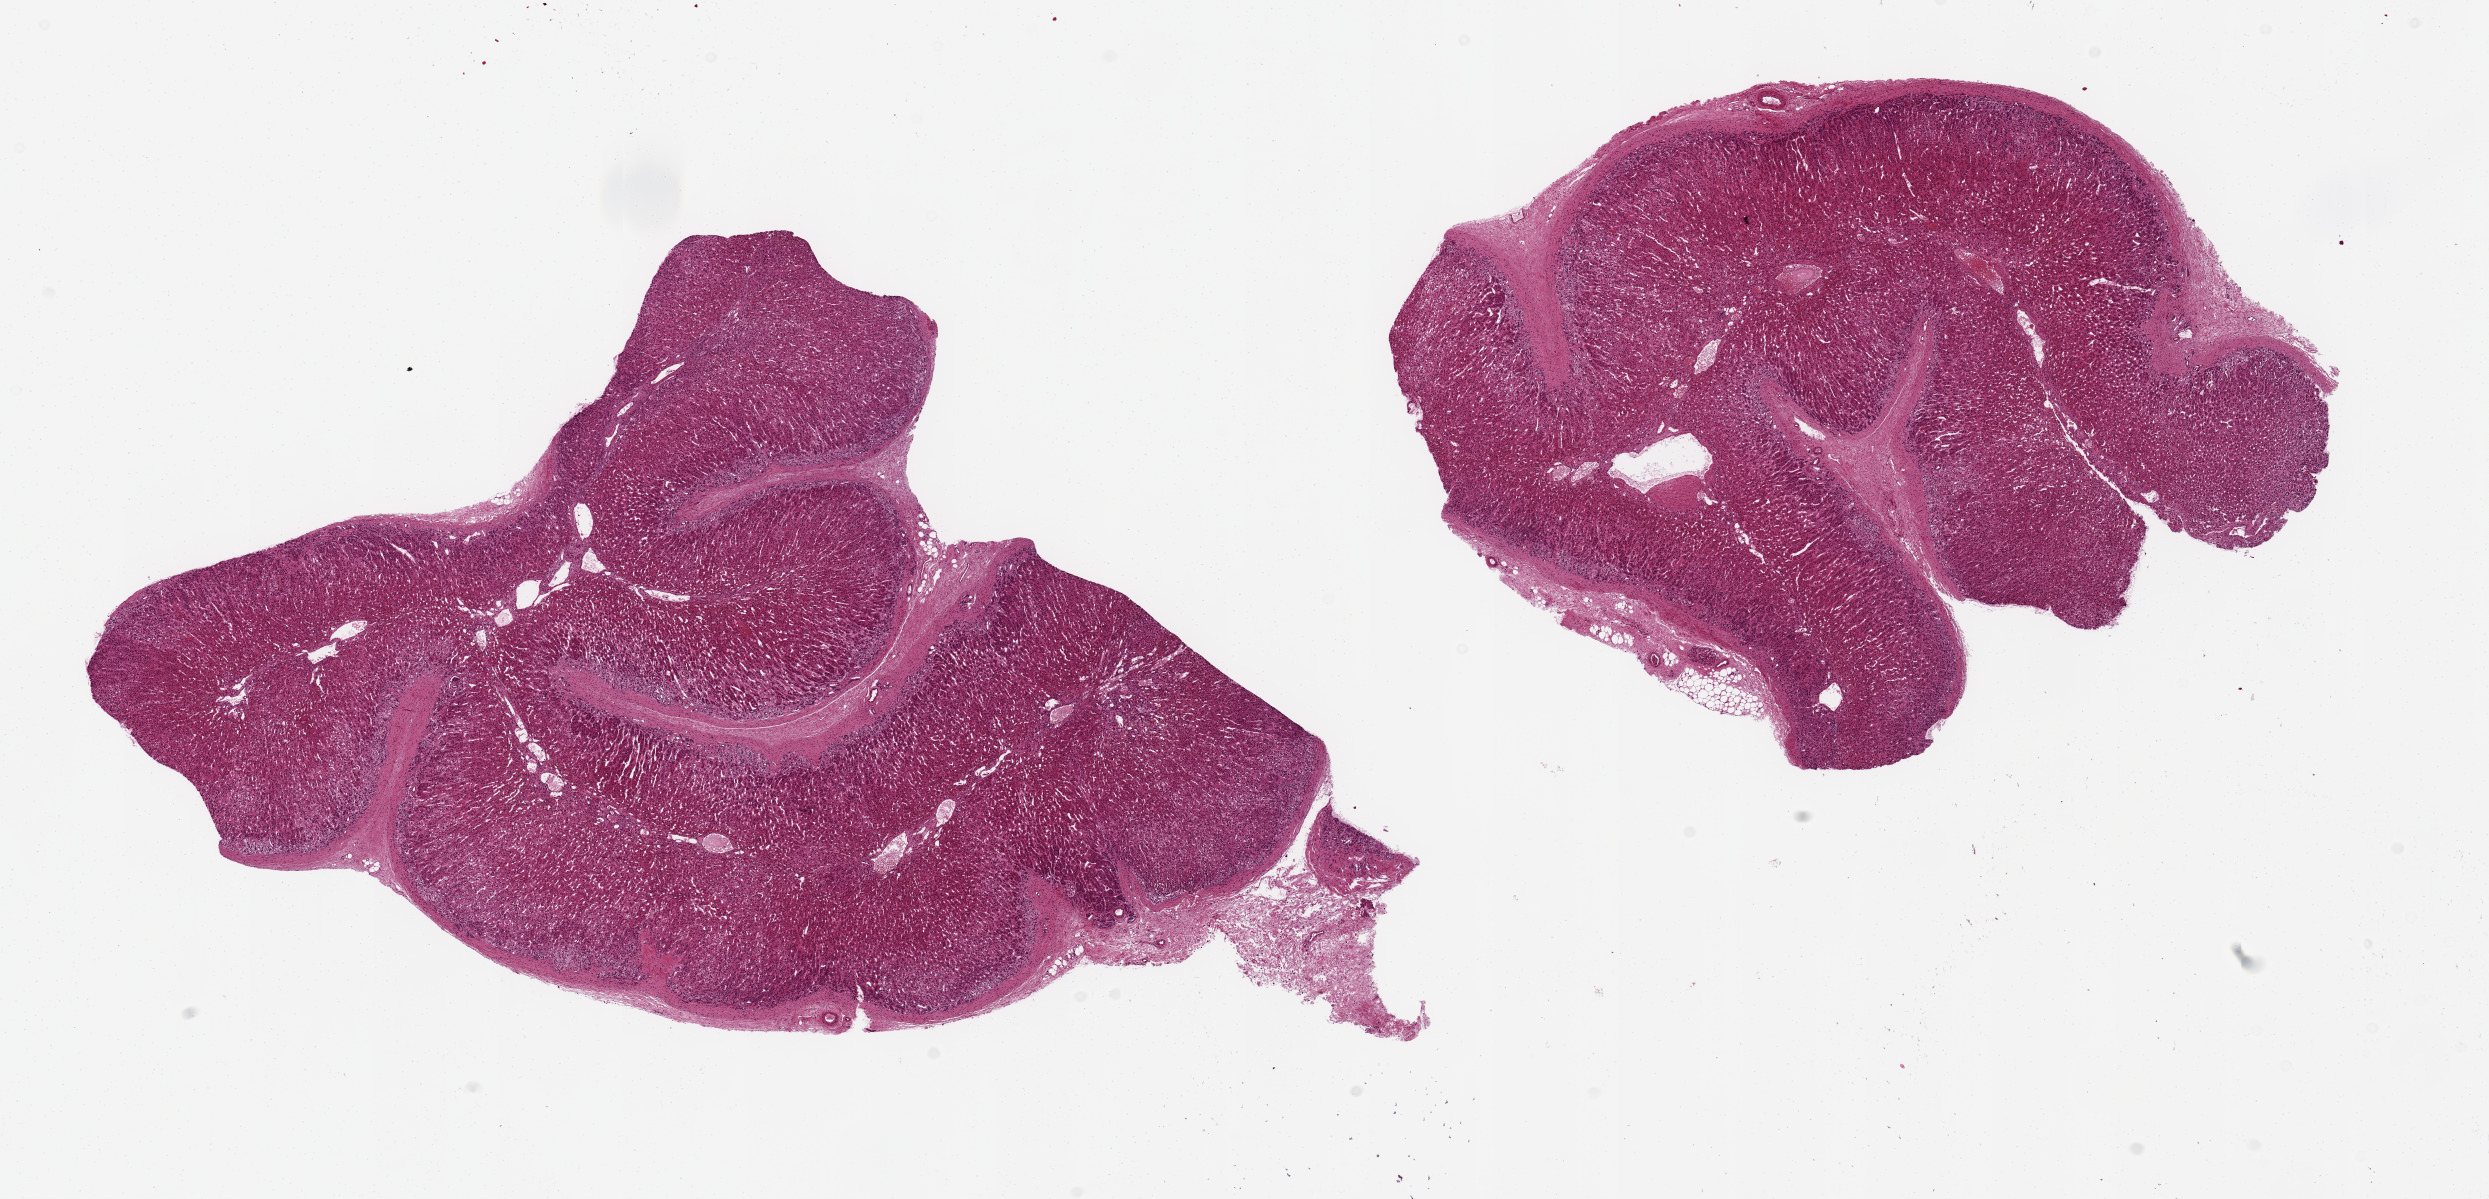
Whole-slide image, hematoxylin and eosin (H&E) stain, brightfield — whole scanned area (about 19.7 x 9.5 mm) shown as a low-resolution overview. PAXgene-fixed paraffin-embedded (PFPE) section. Section of adrenal gland (target tissue). Donor tissue sample. Donor: female.
Pathologist's review note for this sample: 2 ~8.5x6mm aliquots. Cortex only, no visible medulla.